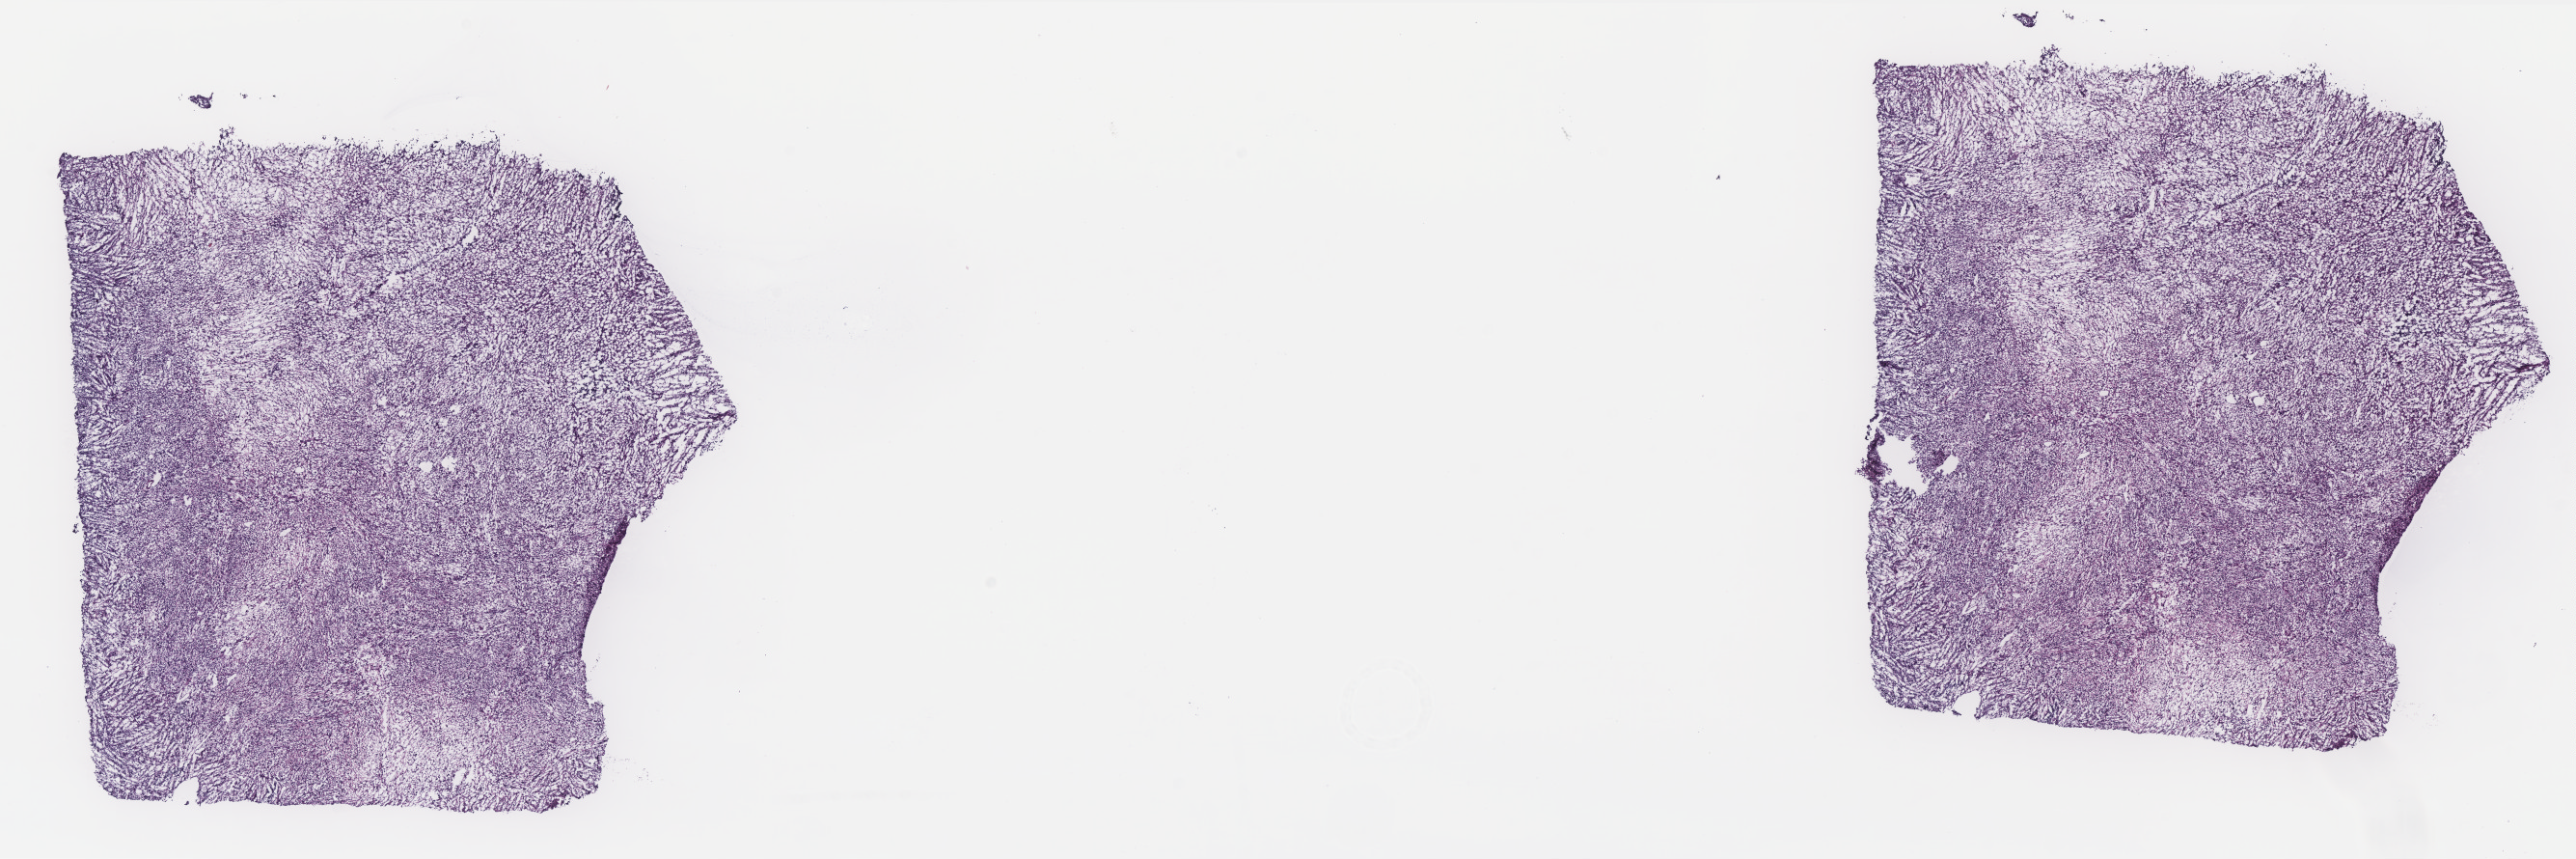
Digitized H&E tissue section (whole slide) — shown as a low-resolution overview of the whole scanned area (about 21.4 x 7.1 mm, acquisition: 40x scan), frozen section from the top of the tissue portion, sample: primary tumour, retroperitoneum and peritoneum. Male patient; age at initial diagnosis 60 years. Slide review estimates, as recorded: tumour cells 90%, tumour nuclei 90%, normal cells 0%, stromal cells 10%, necrosis 0%. Infiltration values recorded for this section: lymphocyte infiltration 2%, monocyte infiltration 1%, neutrophil infiltration 1%.
- pathologic diagnosis: Dedifferentiated liposarcoma (retroperitoneum)